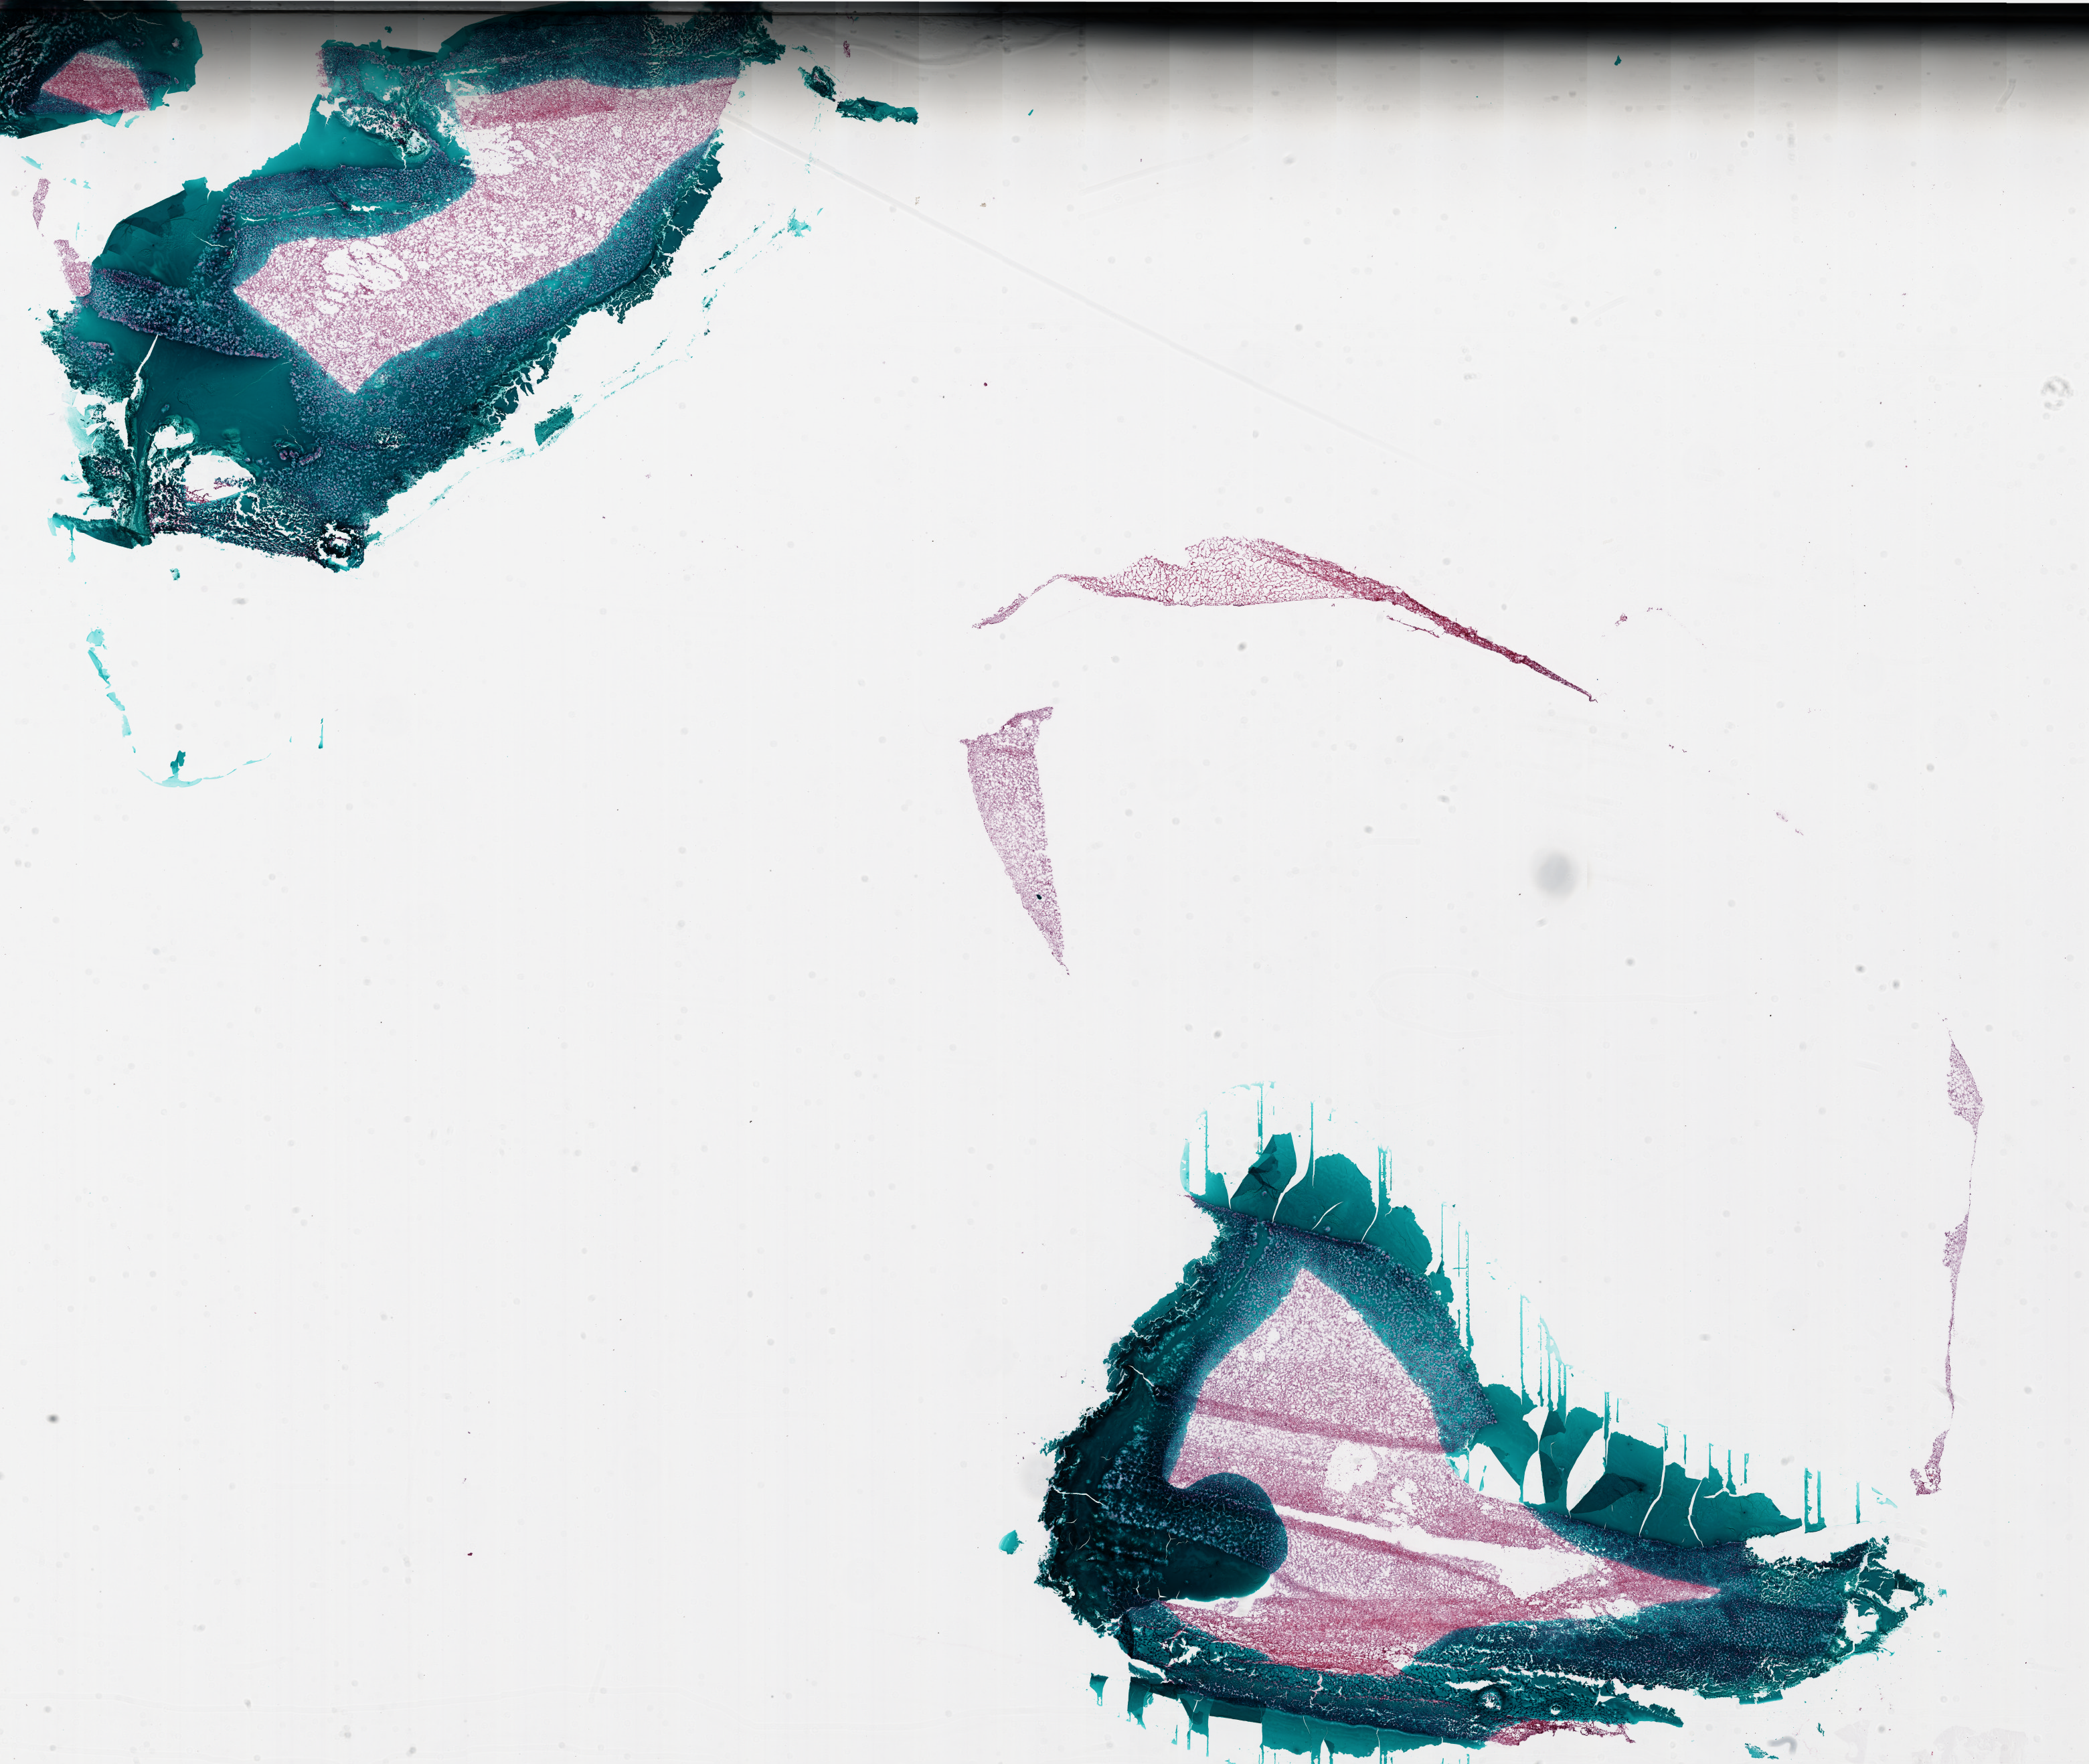
Hematoxylin and eosin (H&E) stained whole-slide image, whole scanned area (about 25.0 x 21.1 mm, acquisition: 20x scan) shown as a low-resolution overview, frozen section from the bottom of the tissue portion, brain, primary tumour sample. Patient: female, age at initial diagnosis 27 years. Composition of this section per pathologist review: tumour cells 100%, tumour nuclei 100%, normal cells 0%, stromal cells 0%, necrosis 0%.
• pathologic diagnosis: Glioblastoma